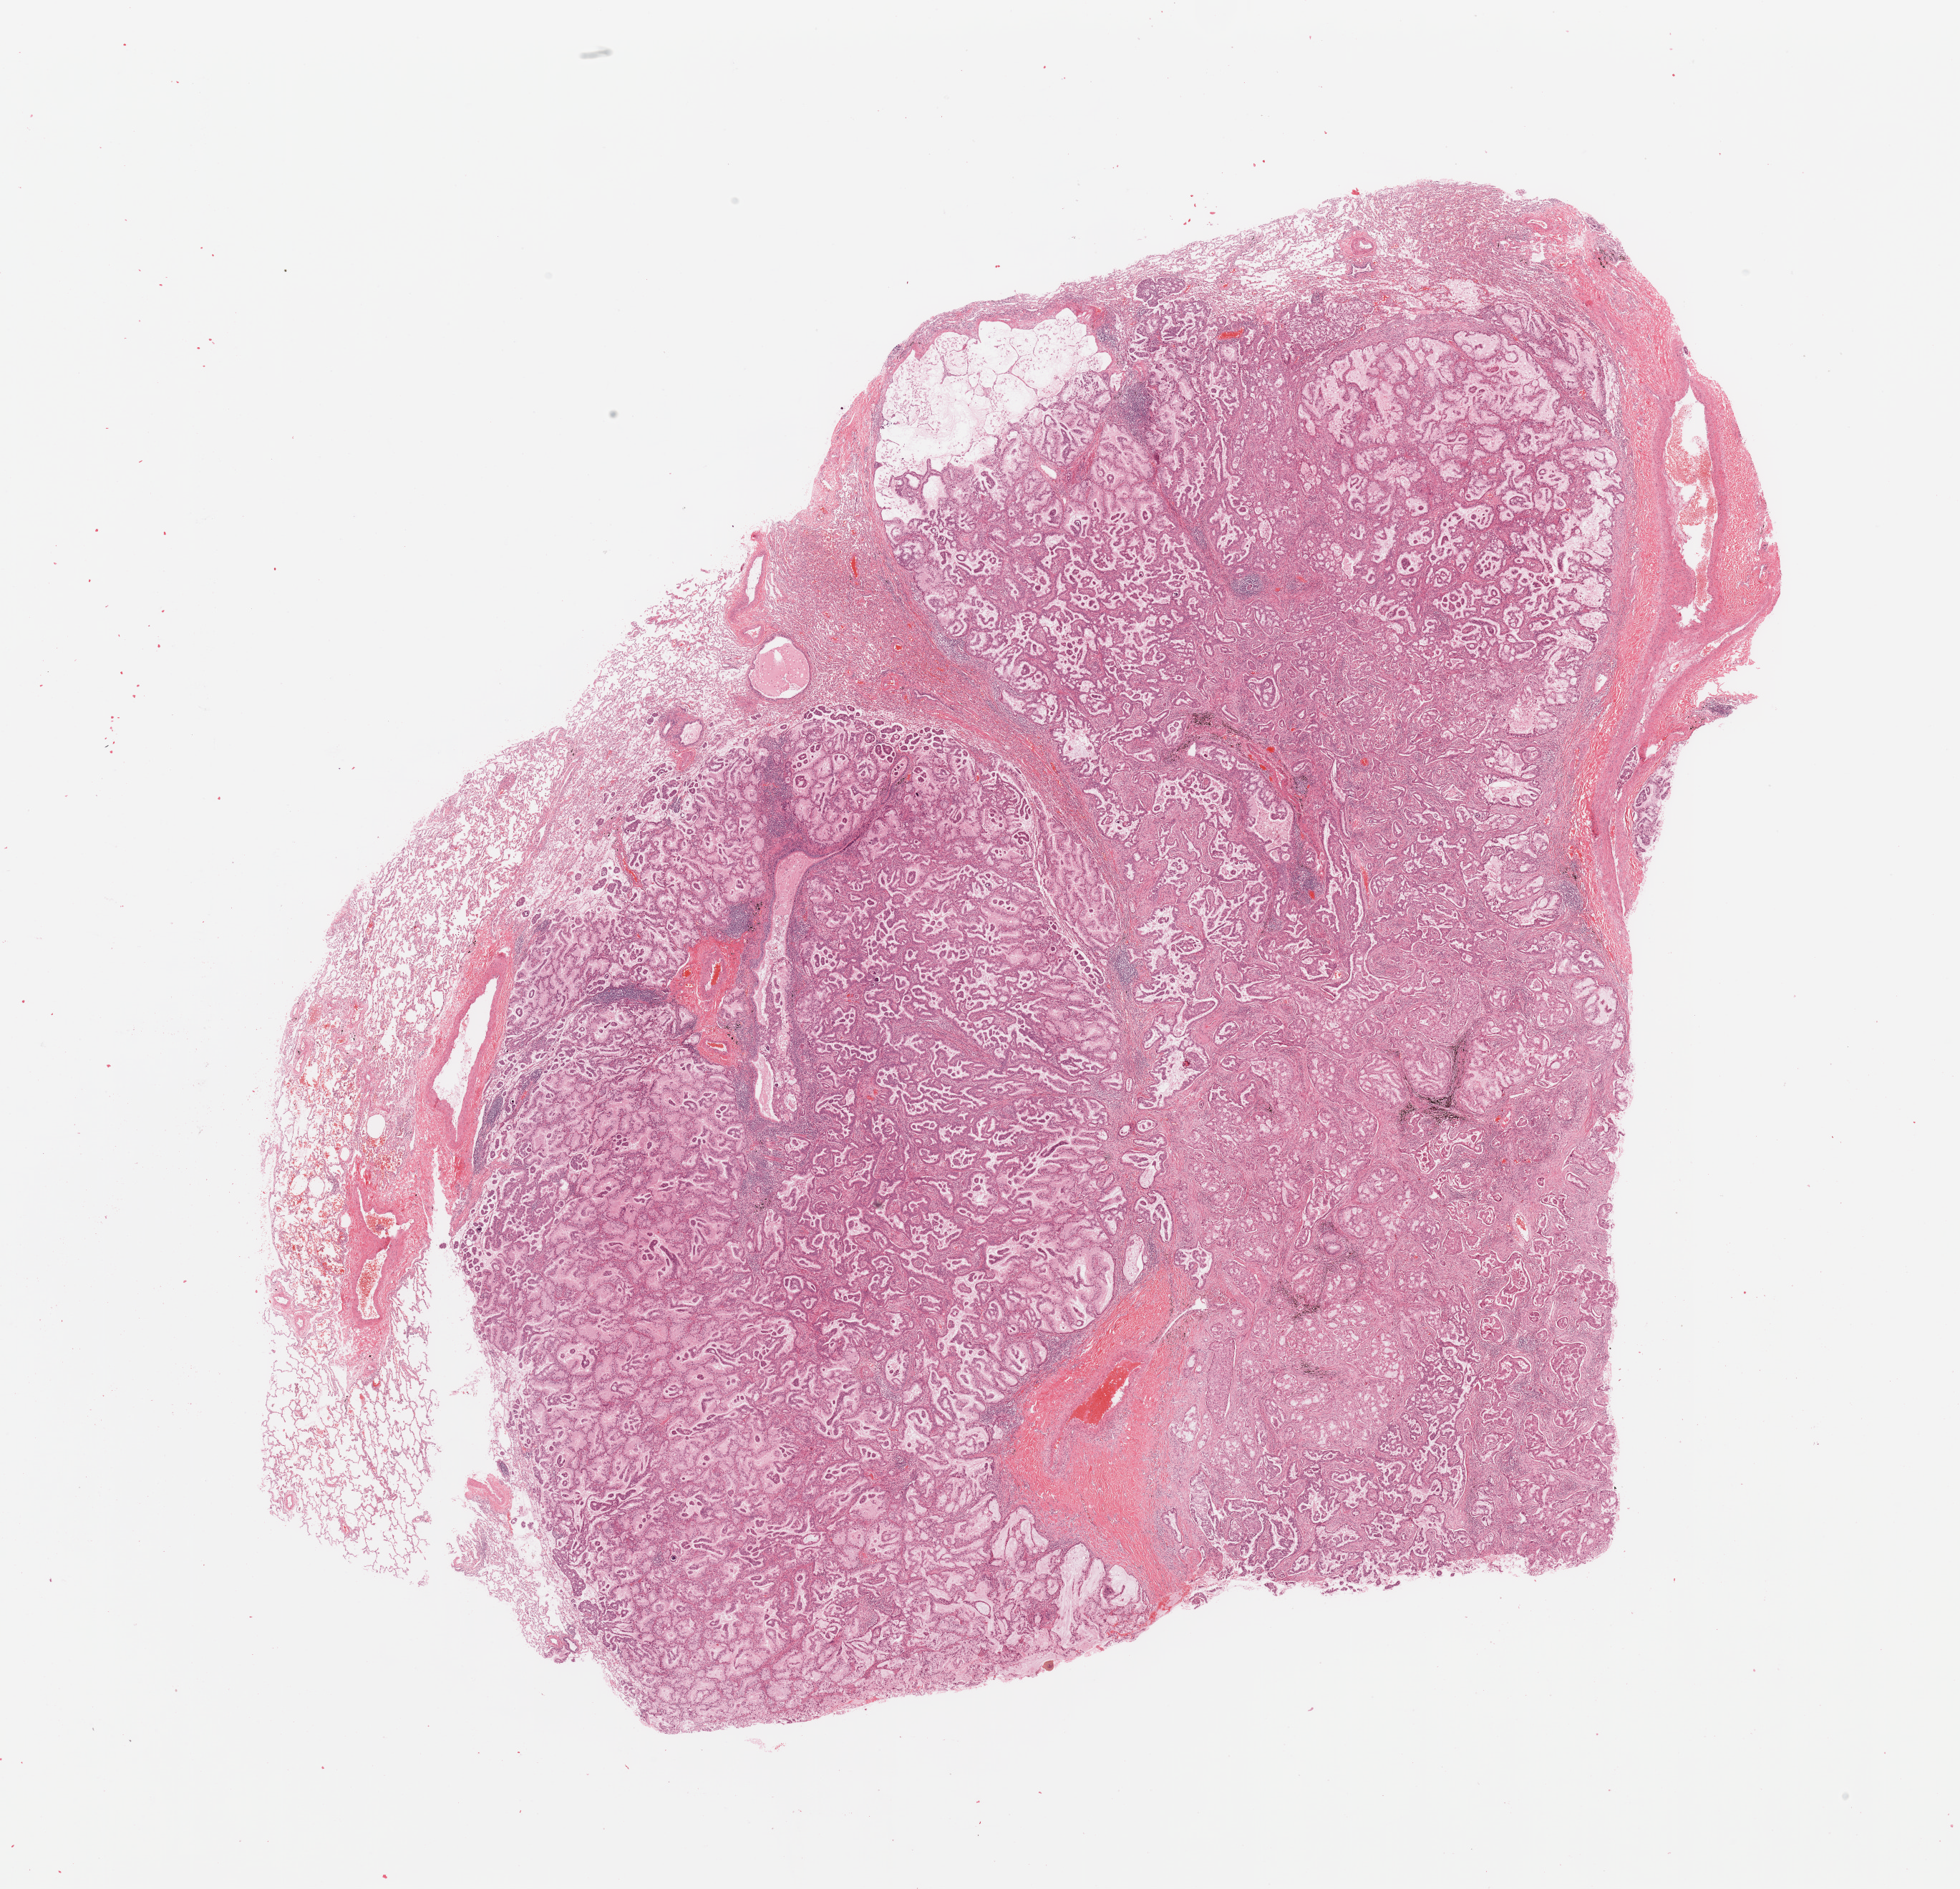
Digitized H&E-stained tissue section (whole slide), shown as a low-resolution overview of the whole scanned area (about 21.7 x 20.9 mm, slide scanned at 20x); tumour tissue sample, lung. Male, 48 y/o. Histologic grade: G2 (moderately differentiated).
- AJCC pathologic stage: IIIA
- histologic diagnosis: Adenocarcinoma, NOS